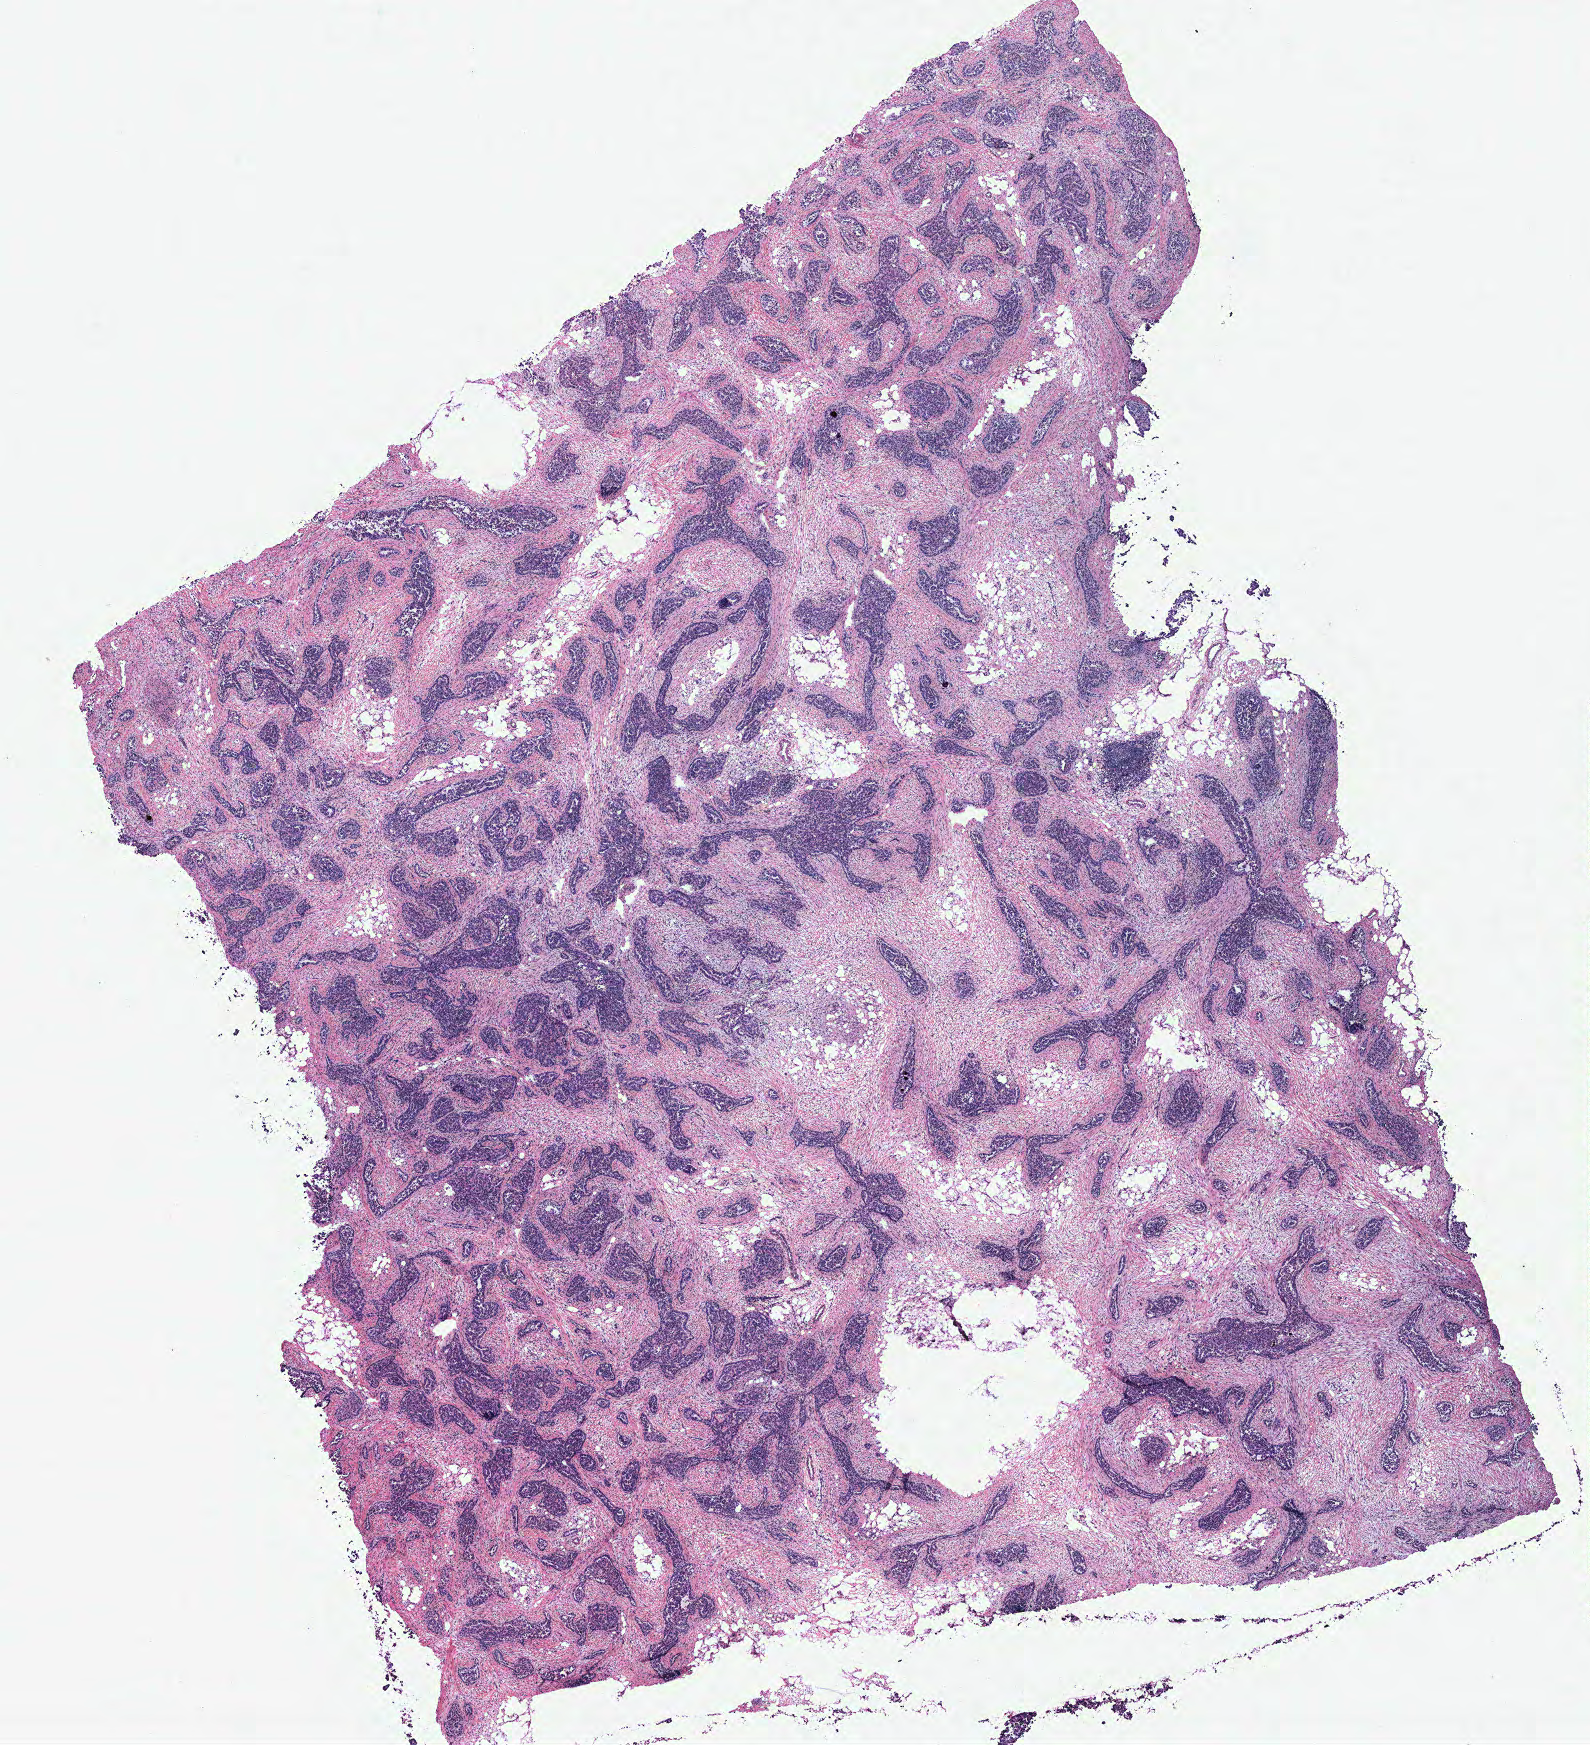
H&E whole-slide image — whole scanned area (about 12.7 x 14.0 mm, acquisition: 40x scan) shown as a low-resolution overview, tumour tissue sample, ovary. Female, 57 y/o.
Diagnosis: Serous adenocarcinoma, NOS. Primary tumour site (as recorded): ovary.